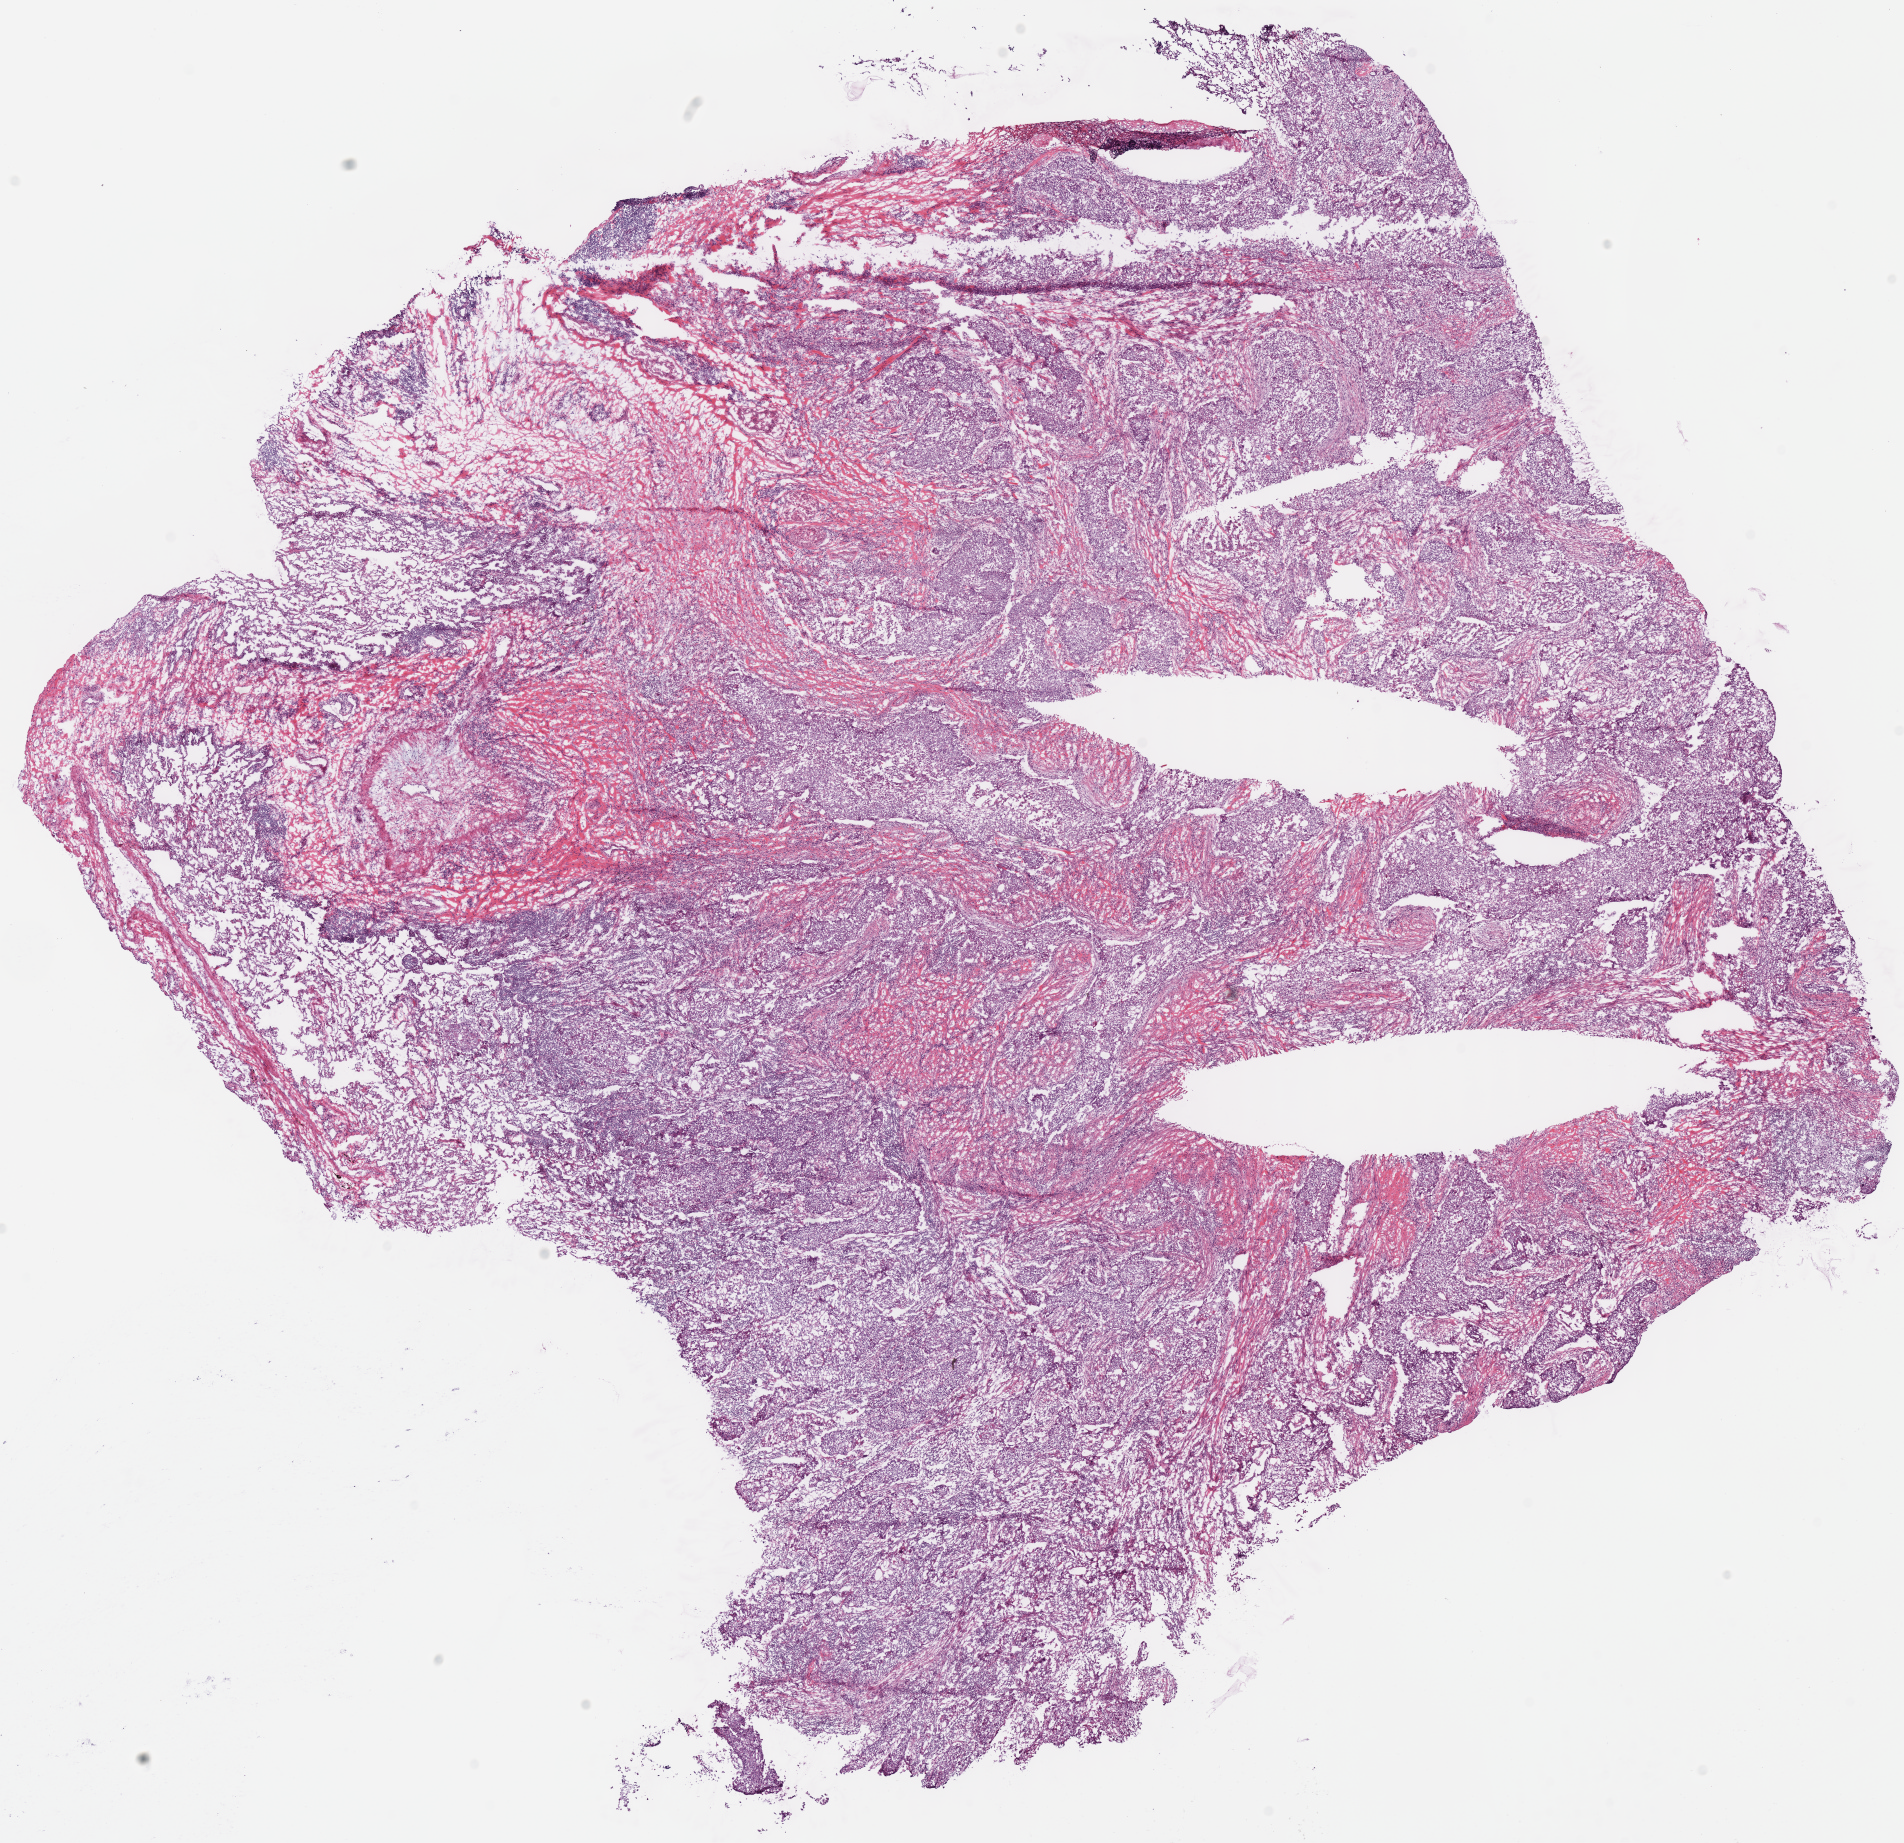
Digitized Hematoxylin and eosin (H&E) stained tissue section (whole slide) — whole scanned area (about 15.0 x 14.5 mm) shown as a low-resolution overview. Frozen section. Sample: primary tumour, lung. Patient: female, age at initial diagnosis 45 years. Composition of this section per pathologist review: tumour cells 75%, tumour nuclei 60%, normal cells 5%, stromal cells 20%, necrosis 0%.
- pathologic diagnosis: Squamous cell carcinoma, NOS (upper lobe, lung)
- AJCC pathologic stage: IIA (7th edition)
- laterality: right